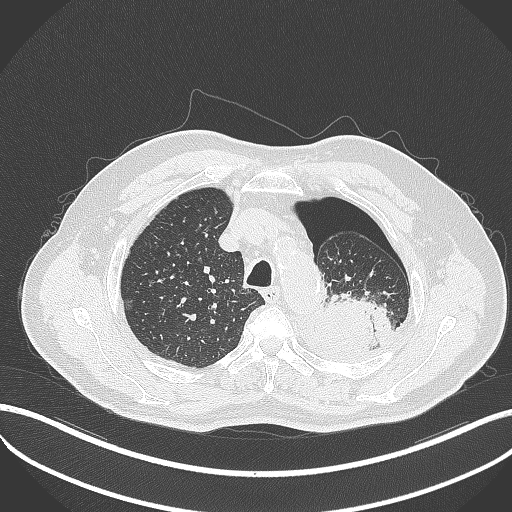
Chest CT, one axial slice. Position 399 of 464 along the scan axis. Reconstruction kernel B70f. 120 kVp. Lung window (W 1500 / L -600 HU). 512 × 512 image matrix, field of view 400 × 400 mm. Patient: male, 76 years. From the clinical record (not read from this slice): clinical TNM (as recorded): T3 N0 M1b.
Annotated regions visible in this slice (rectangle marked by the reading radiologist):
- lung tumour (recorded histology: adenocarcinoma): bounding box [x1, y1, x2, y2] px = [311, 292, 391, 352]